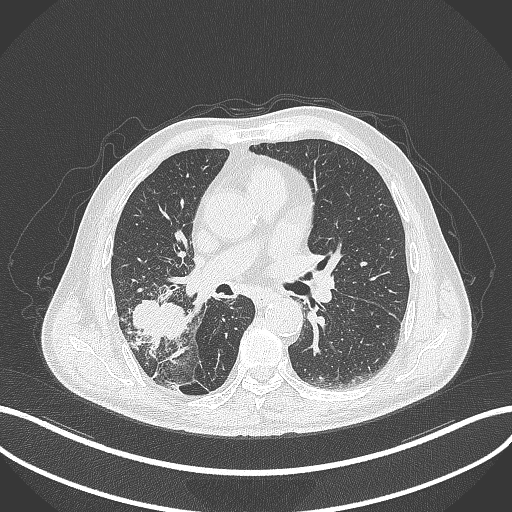
Chest CT, one axial slice. Slice 227 of 429 in the series (ordered by position). Reconstruction kernel B70f. 120 kVp. Lung window (W 1500 / L -600 HU). 1 mm slice thickness. 512 × 512 image matrix, field of view 400 × 400 mm. Patient: male, 72 years. From the clinical record (not read from this slice): clinical TNM (as recorded): T3 N2 M0.
Structures marked on this image (rectangle marked by the reading radiologist):
- lung tumour (recorded histology: adenocarcinoma): bounding box <129,296,188,342> (left, top, right, bottom; pixels)